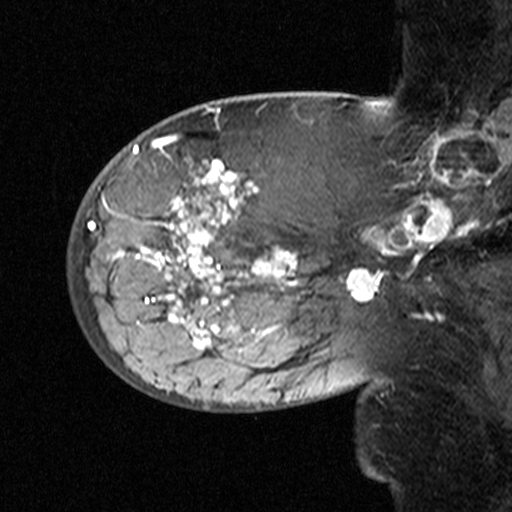
Breast MRI (dynamic contrast-enhanced), one sagittal slice; position 15 of 44 along the scan axis; dynamic contrast-enhanced study with each time point stored as its own series, time point 2 of 3 at this slice position (early post-contrast, ordered by acquisition time); 1.5 T; TE 4.5 ms, TR 11 ms; 3 mm slice thickness; 512 × 512 image matrix. Patient: female, 53 years. Case-level facts recorded for this patient, not image findings: setting: breast cancer imaged before/during neoadjuvant chemotherapy; receptor status: HR-positive, HER2-negative.
Structures marked on this image (semi-automatic segmentation, software-assisted and operator-edited):
- analysis volume of interest (the breast-tissue region the enhancement analysis was run in; not a lesion): bounding box [x1, y1, x2, y2] px = [76, 140, 311, 353]
- tumour enhancement mask (voxels above the 90 % enhancement threshold inside the analysis volume of interest): [117, 159, 297, 348]